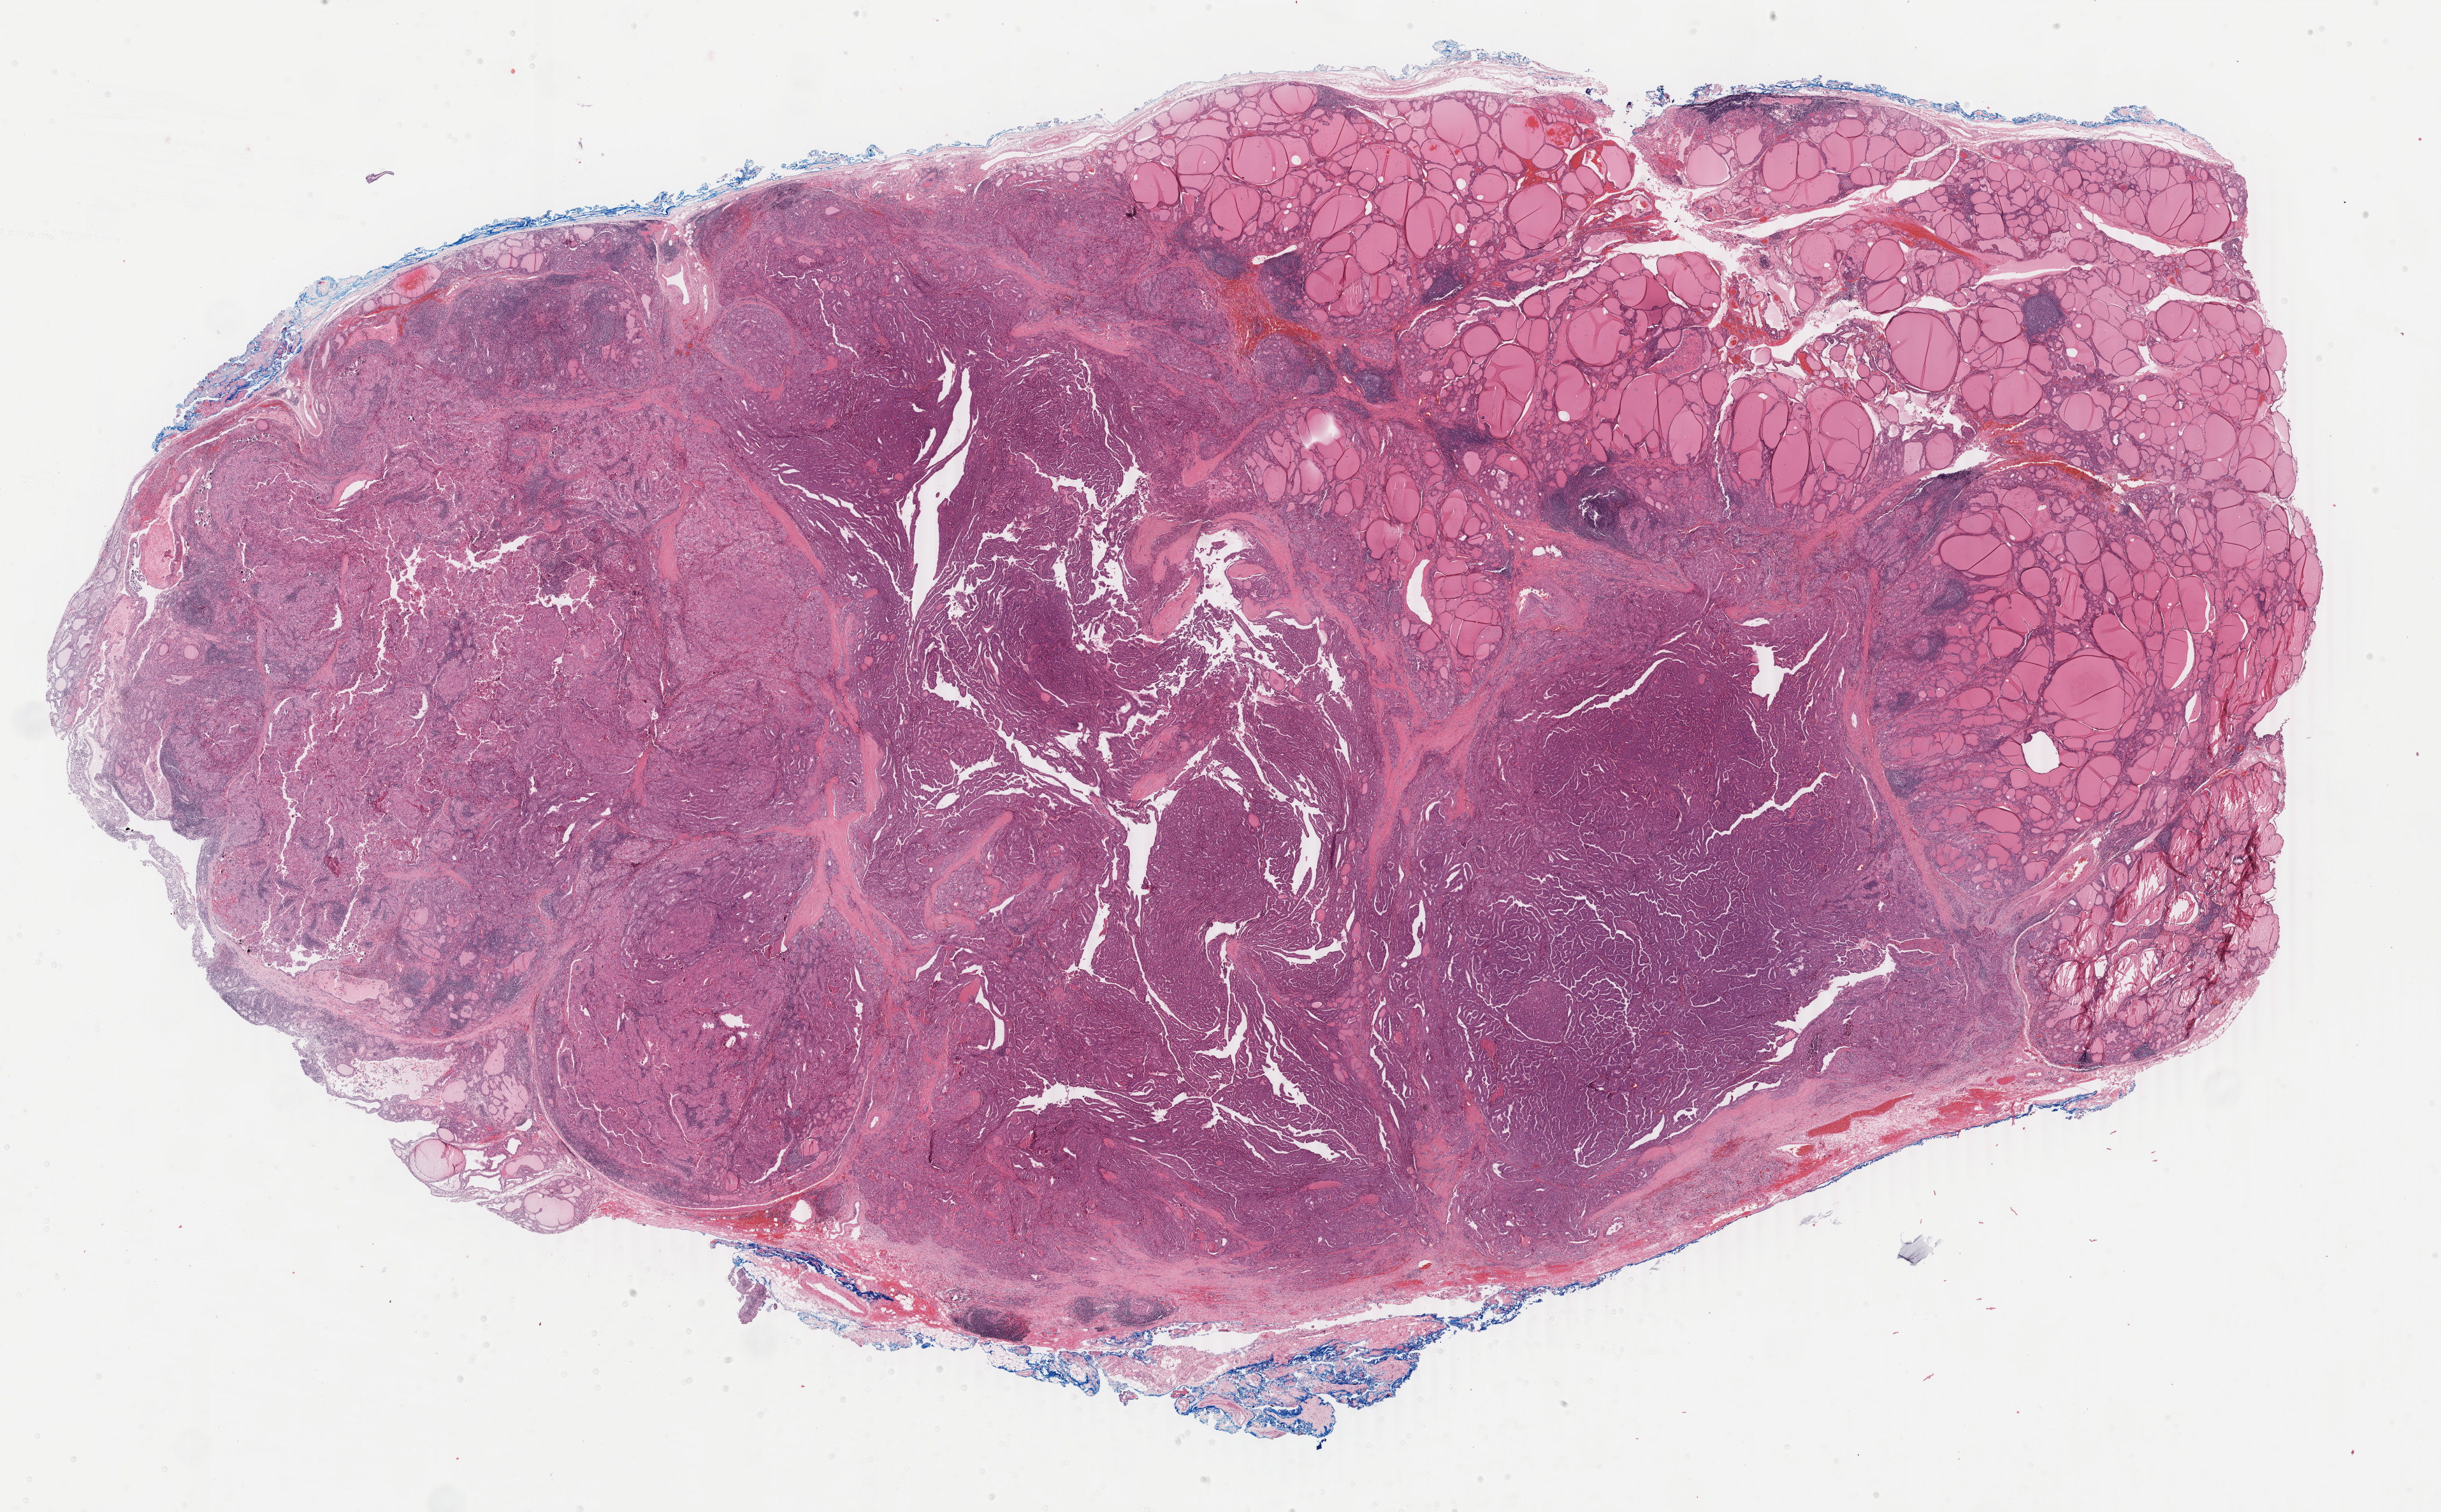
H&E whole-slide image, low-resolution overview of the scanned area, about 30.5 x 18.9 mm (acquisition: 40x scan), formalin-fixed paraffin-embedded (FFPE) diagnostic section, sample: primary tumour, thyroid. Patient: female, age at initial diagnosis 44 years.
AJCC pathologic stage: I (6th edition). Diagnosis: Papillary adenocarcinoma, NOS (thyroid gland).